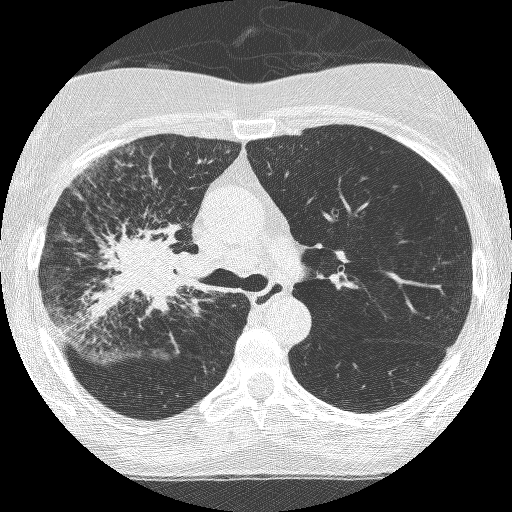
Axial slice from a low-dose chest CT screening exam, third annual screen, lung window (W 1500 / L -600 HU), 1.25 mm slice thickness, lung (sharp) reconstruction kernel (BONE), 512 × 512 image matrix. Female participant, aged 64 years at enrolment. Former smoker at enrolment.
Expert-annotated lung lesion, bounding box [x1, y1, x2, y2] px = [87, 215, 205, 333]. The exam's reader record, not a measurement of the box and not confirmed to be the same lesion: non-calcified nodule or mass ≥4 mm, right upper lobe, 49 × 43 mm, spiculated (stellate) margins, soft tissue attenuation, pre-existing on the prior screen: yes; interval growth: yes. Later outcome: lung cancer diagnosed 7 days after this screen — adenocarcinoma, NOS, right upper lobe, right middle lobe, right hilum, stage IV (AJCC 6th edition), 85 mm at pathology.